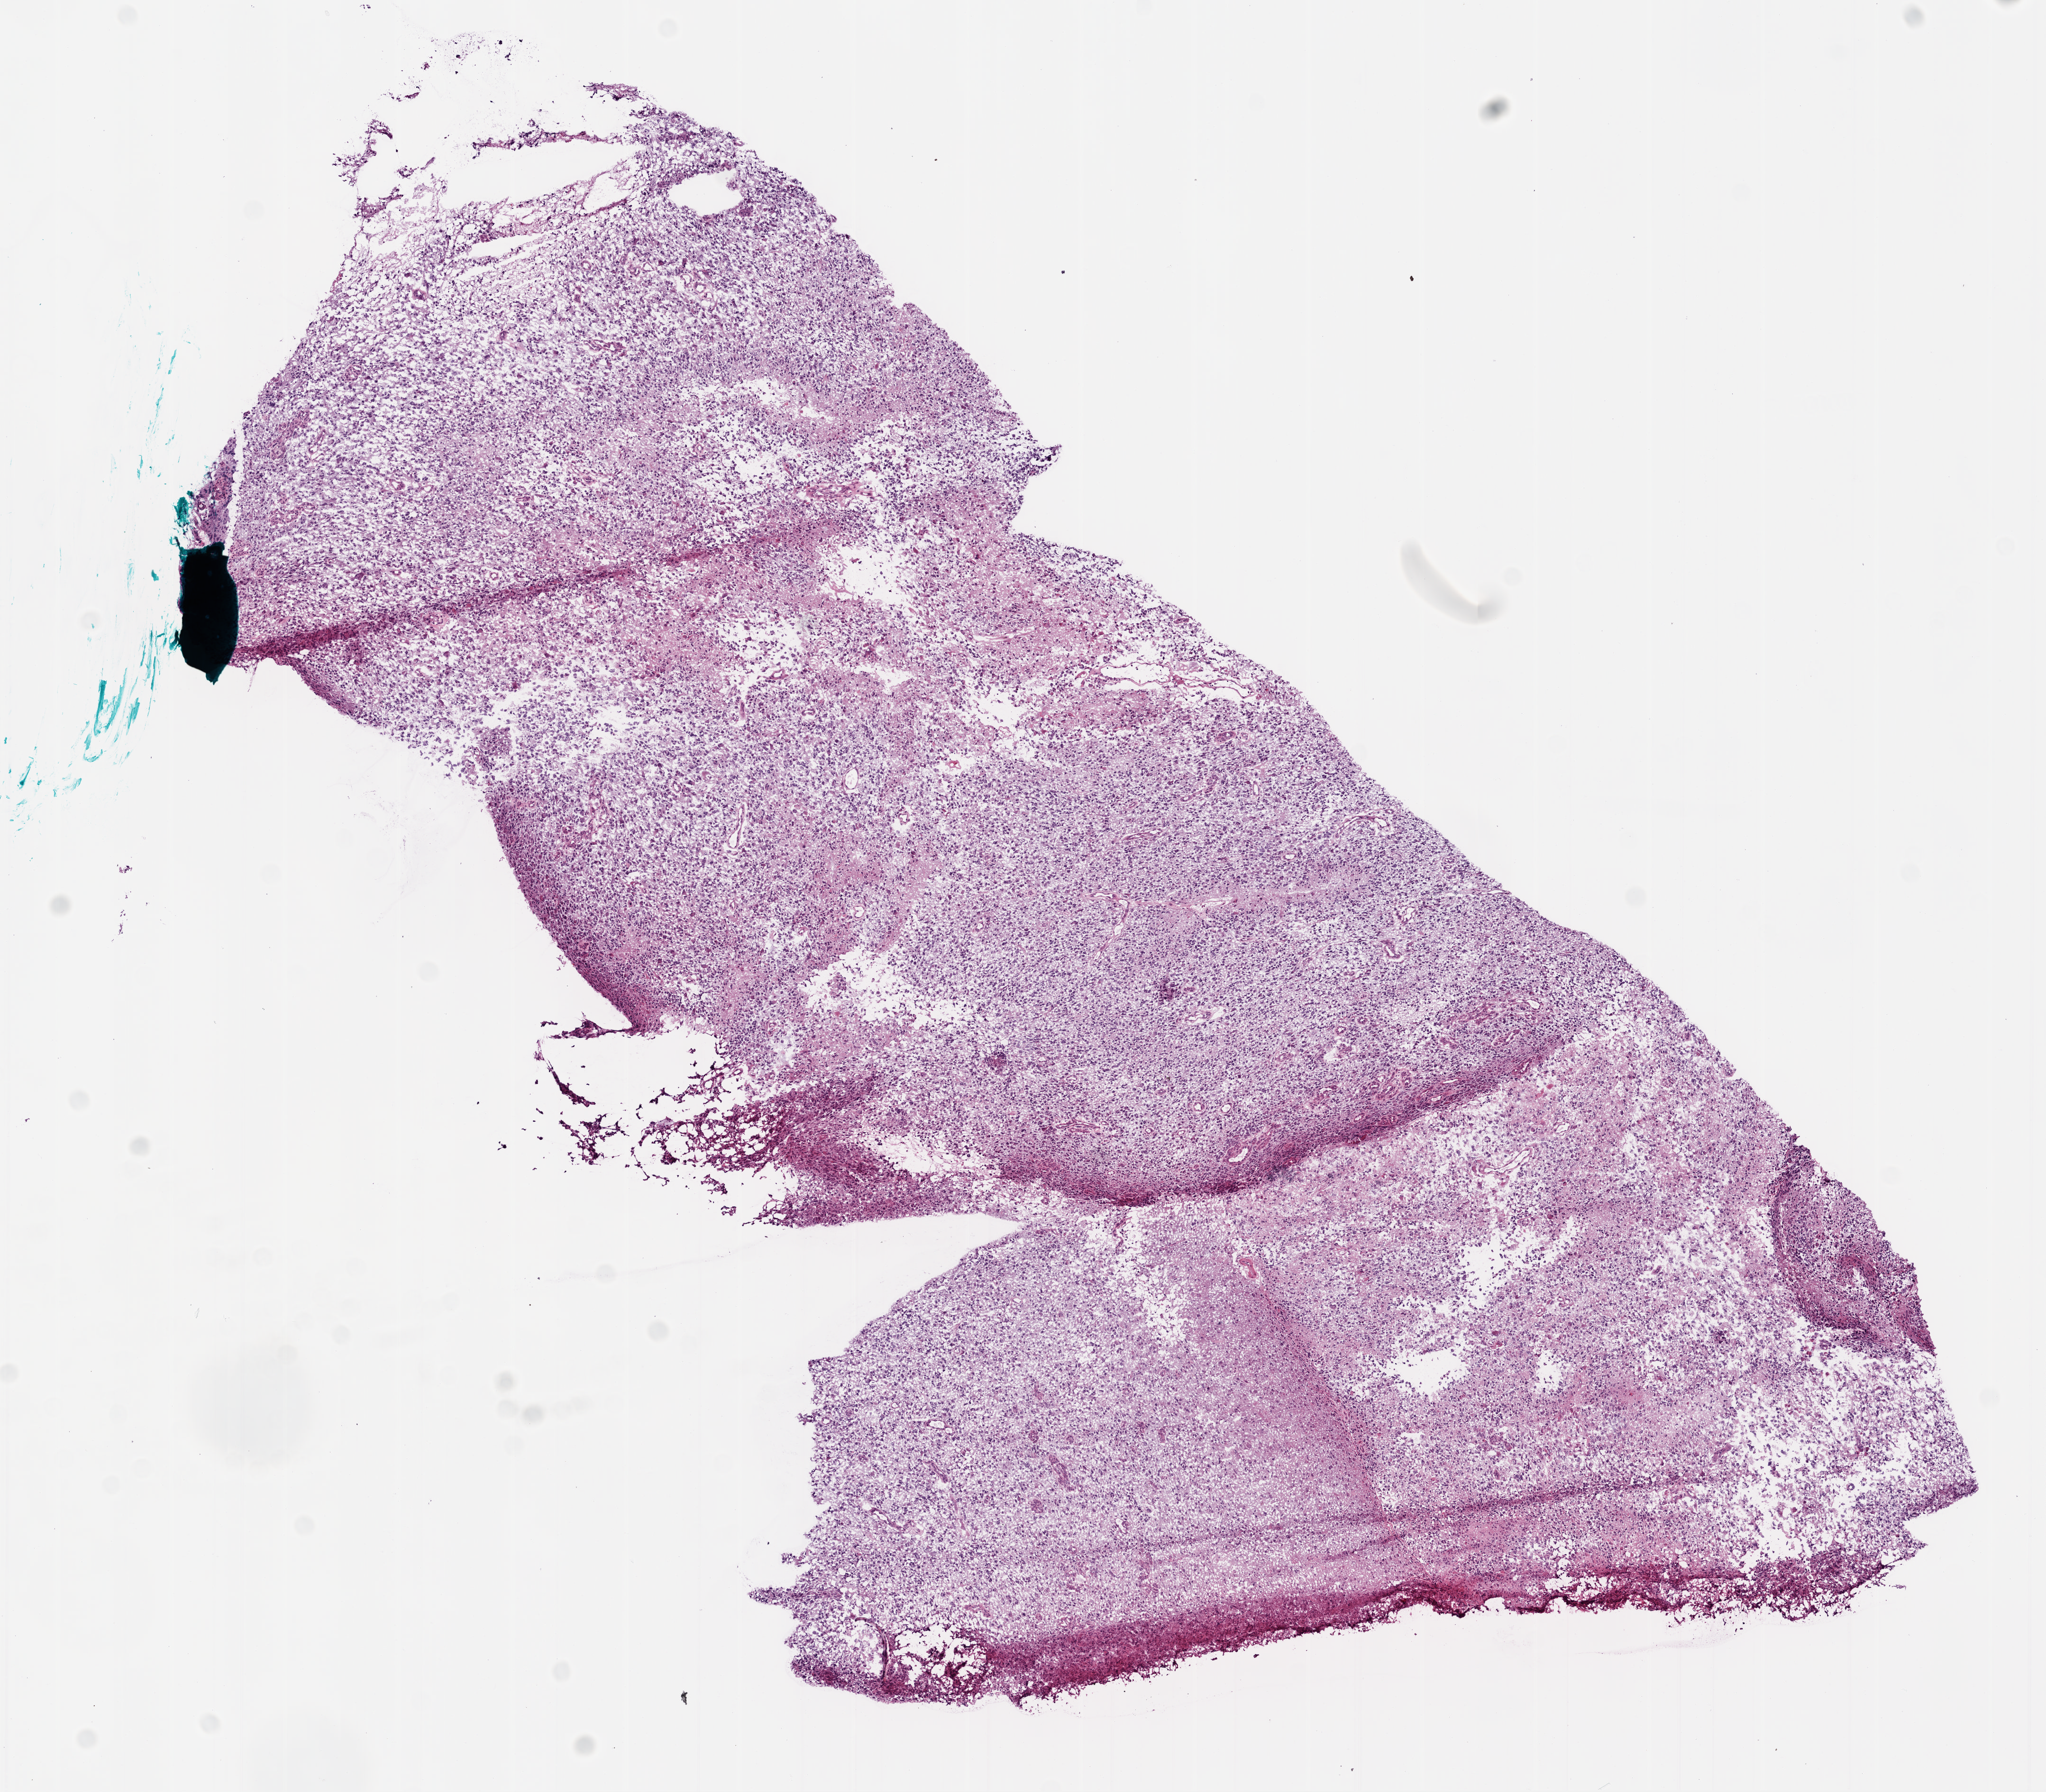
H&E whole-slide image, shown as a low-resolution overview of the whole scanned area (about 8.7 x 7.6 mm, acquisition: 20x scan), frozen section from the bottom of the tissue portion, primary tumour sample from the brain. Male patient; age at initial diagnosis 77 years. Pathologist review of this section (percent, as recorded): tumour cells 90%, tumour nuclei 100%, normal cells 0%, stromal cells 0%, necrosis 10%.
* diagnosis: Glioblastoma